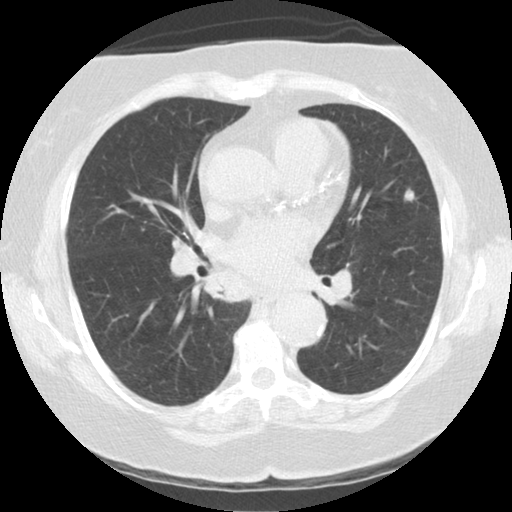
Low-dose screening chest CT, one axial slice. Slice 71 of 122 in the series (ordered by position). Reconstruction kernel STANDARD. Lung window (W 1500 / L -600 HU). 2.5 mm slice thickness. 512 × 512 image matrix, field of view 329 × 329 mm.
Annotated regions visible in this slice (expert manual segmentation):
- lesion 2 (nodule, upper lobe of left lung): bounding box (x1, y1, x2, y2) in pixels: (404, 188, 415, 202)